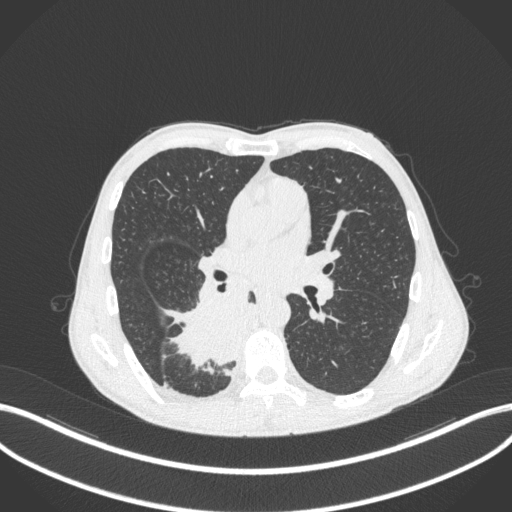
Chest CT, one axial slice; slice 198 of 371 in the series (ordered by position); 120 kVp; lung window (W 1500 / L -600 HU); 512 × 512 image matrix, field of view 400 × 400 mm. Patient: male, 58 years. Case-level facts recorded for this patient, not image findings: clinical TNM (as recorded): T3 N1 M1.
Structures marked on this image (bounding box drawn by a radiologist):
- lung tumour (recorded histology: squamous cell carcinoma): bounding box [x1, y1, x2, y2] px = [162, 283, 261, 368]